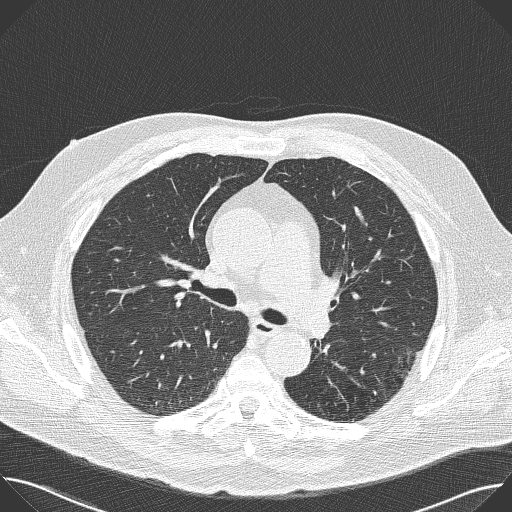
Low-dose screening chest CT, axial slice. First (baseline) screen. Lung window (W 1500 / L -600 HU). Lung (sharp) reconstruction kernel (B50f). 120 kVp. 512 × 512 image matrix, field of view 380 × 380 mm. Male participant, aged 68 years at enrolment. Former smoker at enrolment.
Lesion marked by an expert reader, box from (x=376, y=340) to (x=432, y=390) px. The screening reader recorded 2 non-calcified nodules or masses ≥4 mm on this exam; which of them this box marks is not recorded. Lung cancer was diagnosed 512 days after this screen (after the second annual screen): adenocarcinoma, NOS, left lower lobe, poorly differentiated (G3), stage IB (AJCC 6th edition), 17 mm at pathology.